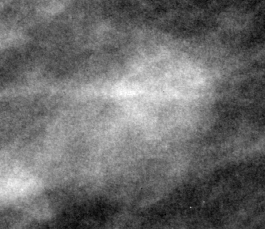
Cropped region of a digitized screen-film mammogram centred on a radiologist-marked abnormality, right breast, MLO view, BI-RADS breast density category 2 (scale 1–4).
Finding: mass, shape lobulated, margins circumscribed / obscured; BI-RADS assessment category 4; pathology (as recorded): benign.